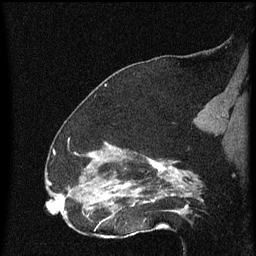
Breast MRI (dynamic contrast-enhanced), one sagittal slice; position 37 of 60 along the scan axis; dynamic contrast-enhanced series, image 2 of 4 at this slice position (ordered by acquisition); 1.5 T; TE 4.2 ms, TR 8 ms; 256 × 256 image matrix, field of view 180 × 180 mm. Female patient, age 52 years.
Annotated regions visible in this slice (semi-automatically segmented with operator editing):
- analysis volume of interest (the breast-tissue region the enhancement analysis was run in; not a lesion): bounding box <73,148,172,219> (left, top, right, bottom; pixels)
- tumour enhancement mask (voxels above the 70 % enhancement threshold inside the analysis volume of interest): <87,158,172,219>